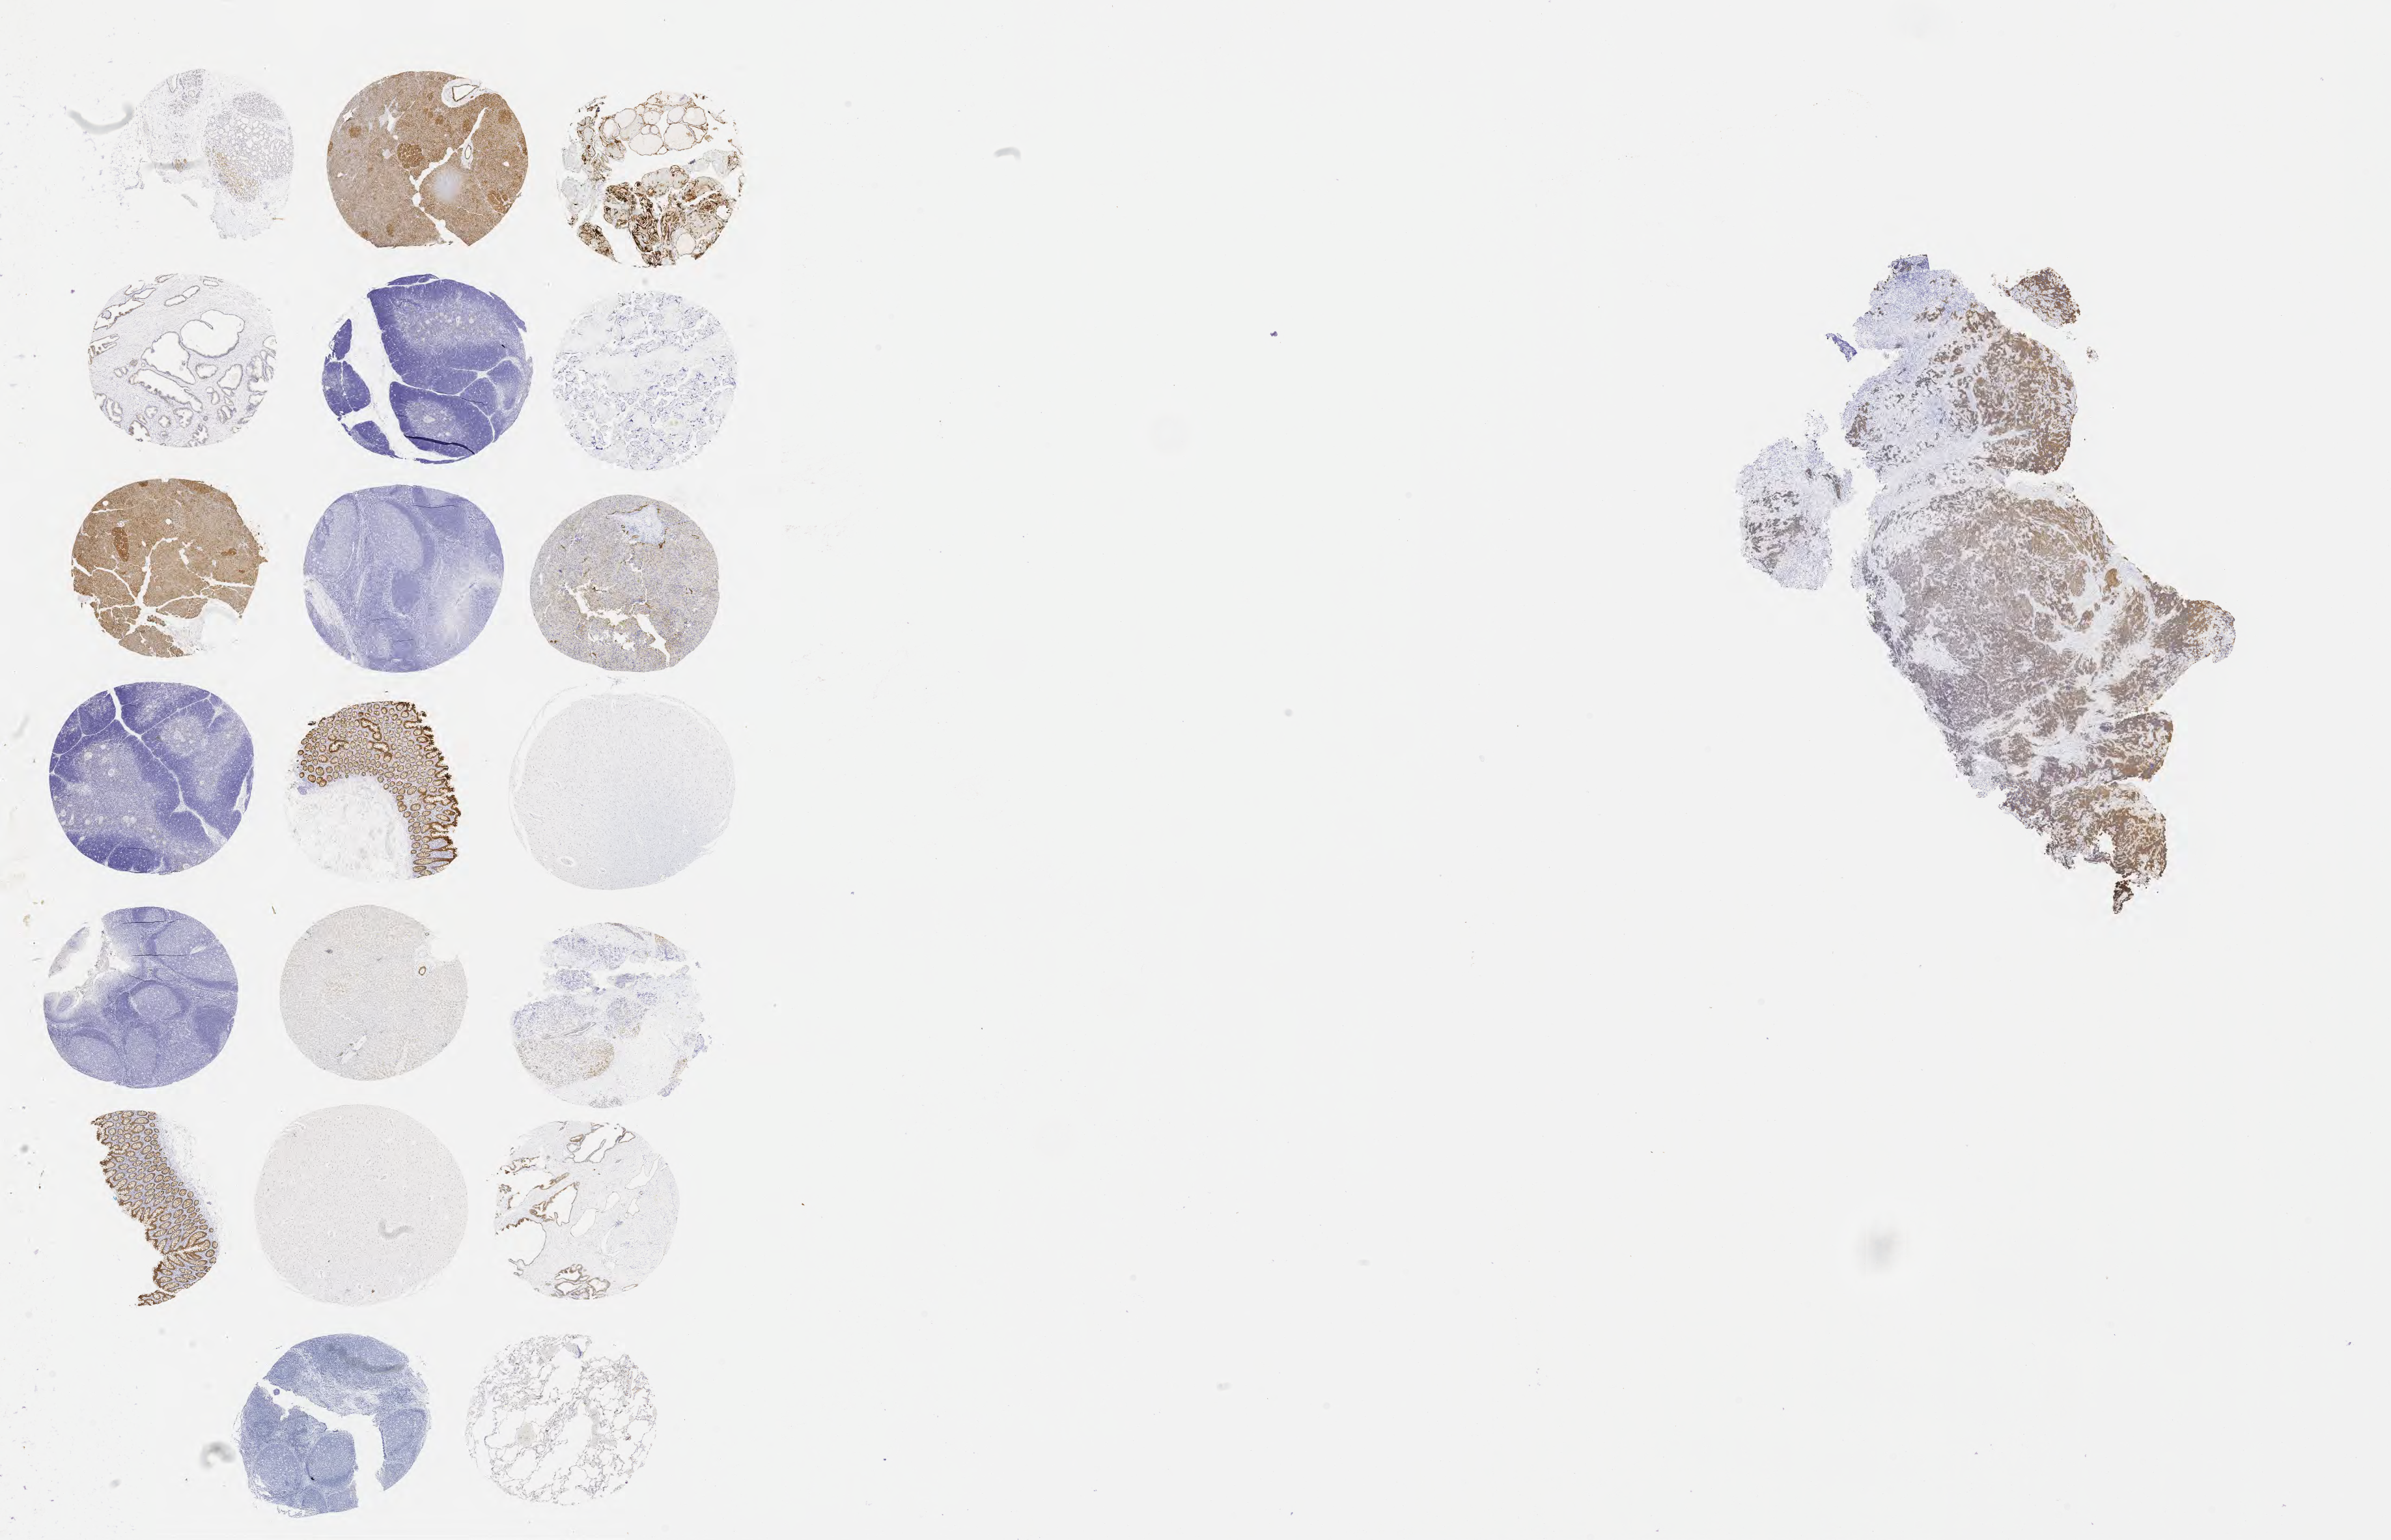
IHC for MOC-31 (anti-EpCAM), whole-slide image — whole scanned area (about 29.7 x 19.1 mm) shown as a low-resolution overview, specimen: tumor tissue, site: cervix. Patient: female, 43 years old.
Diagnosis: Lymphoepithelial carcinoma.